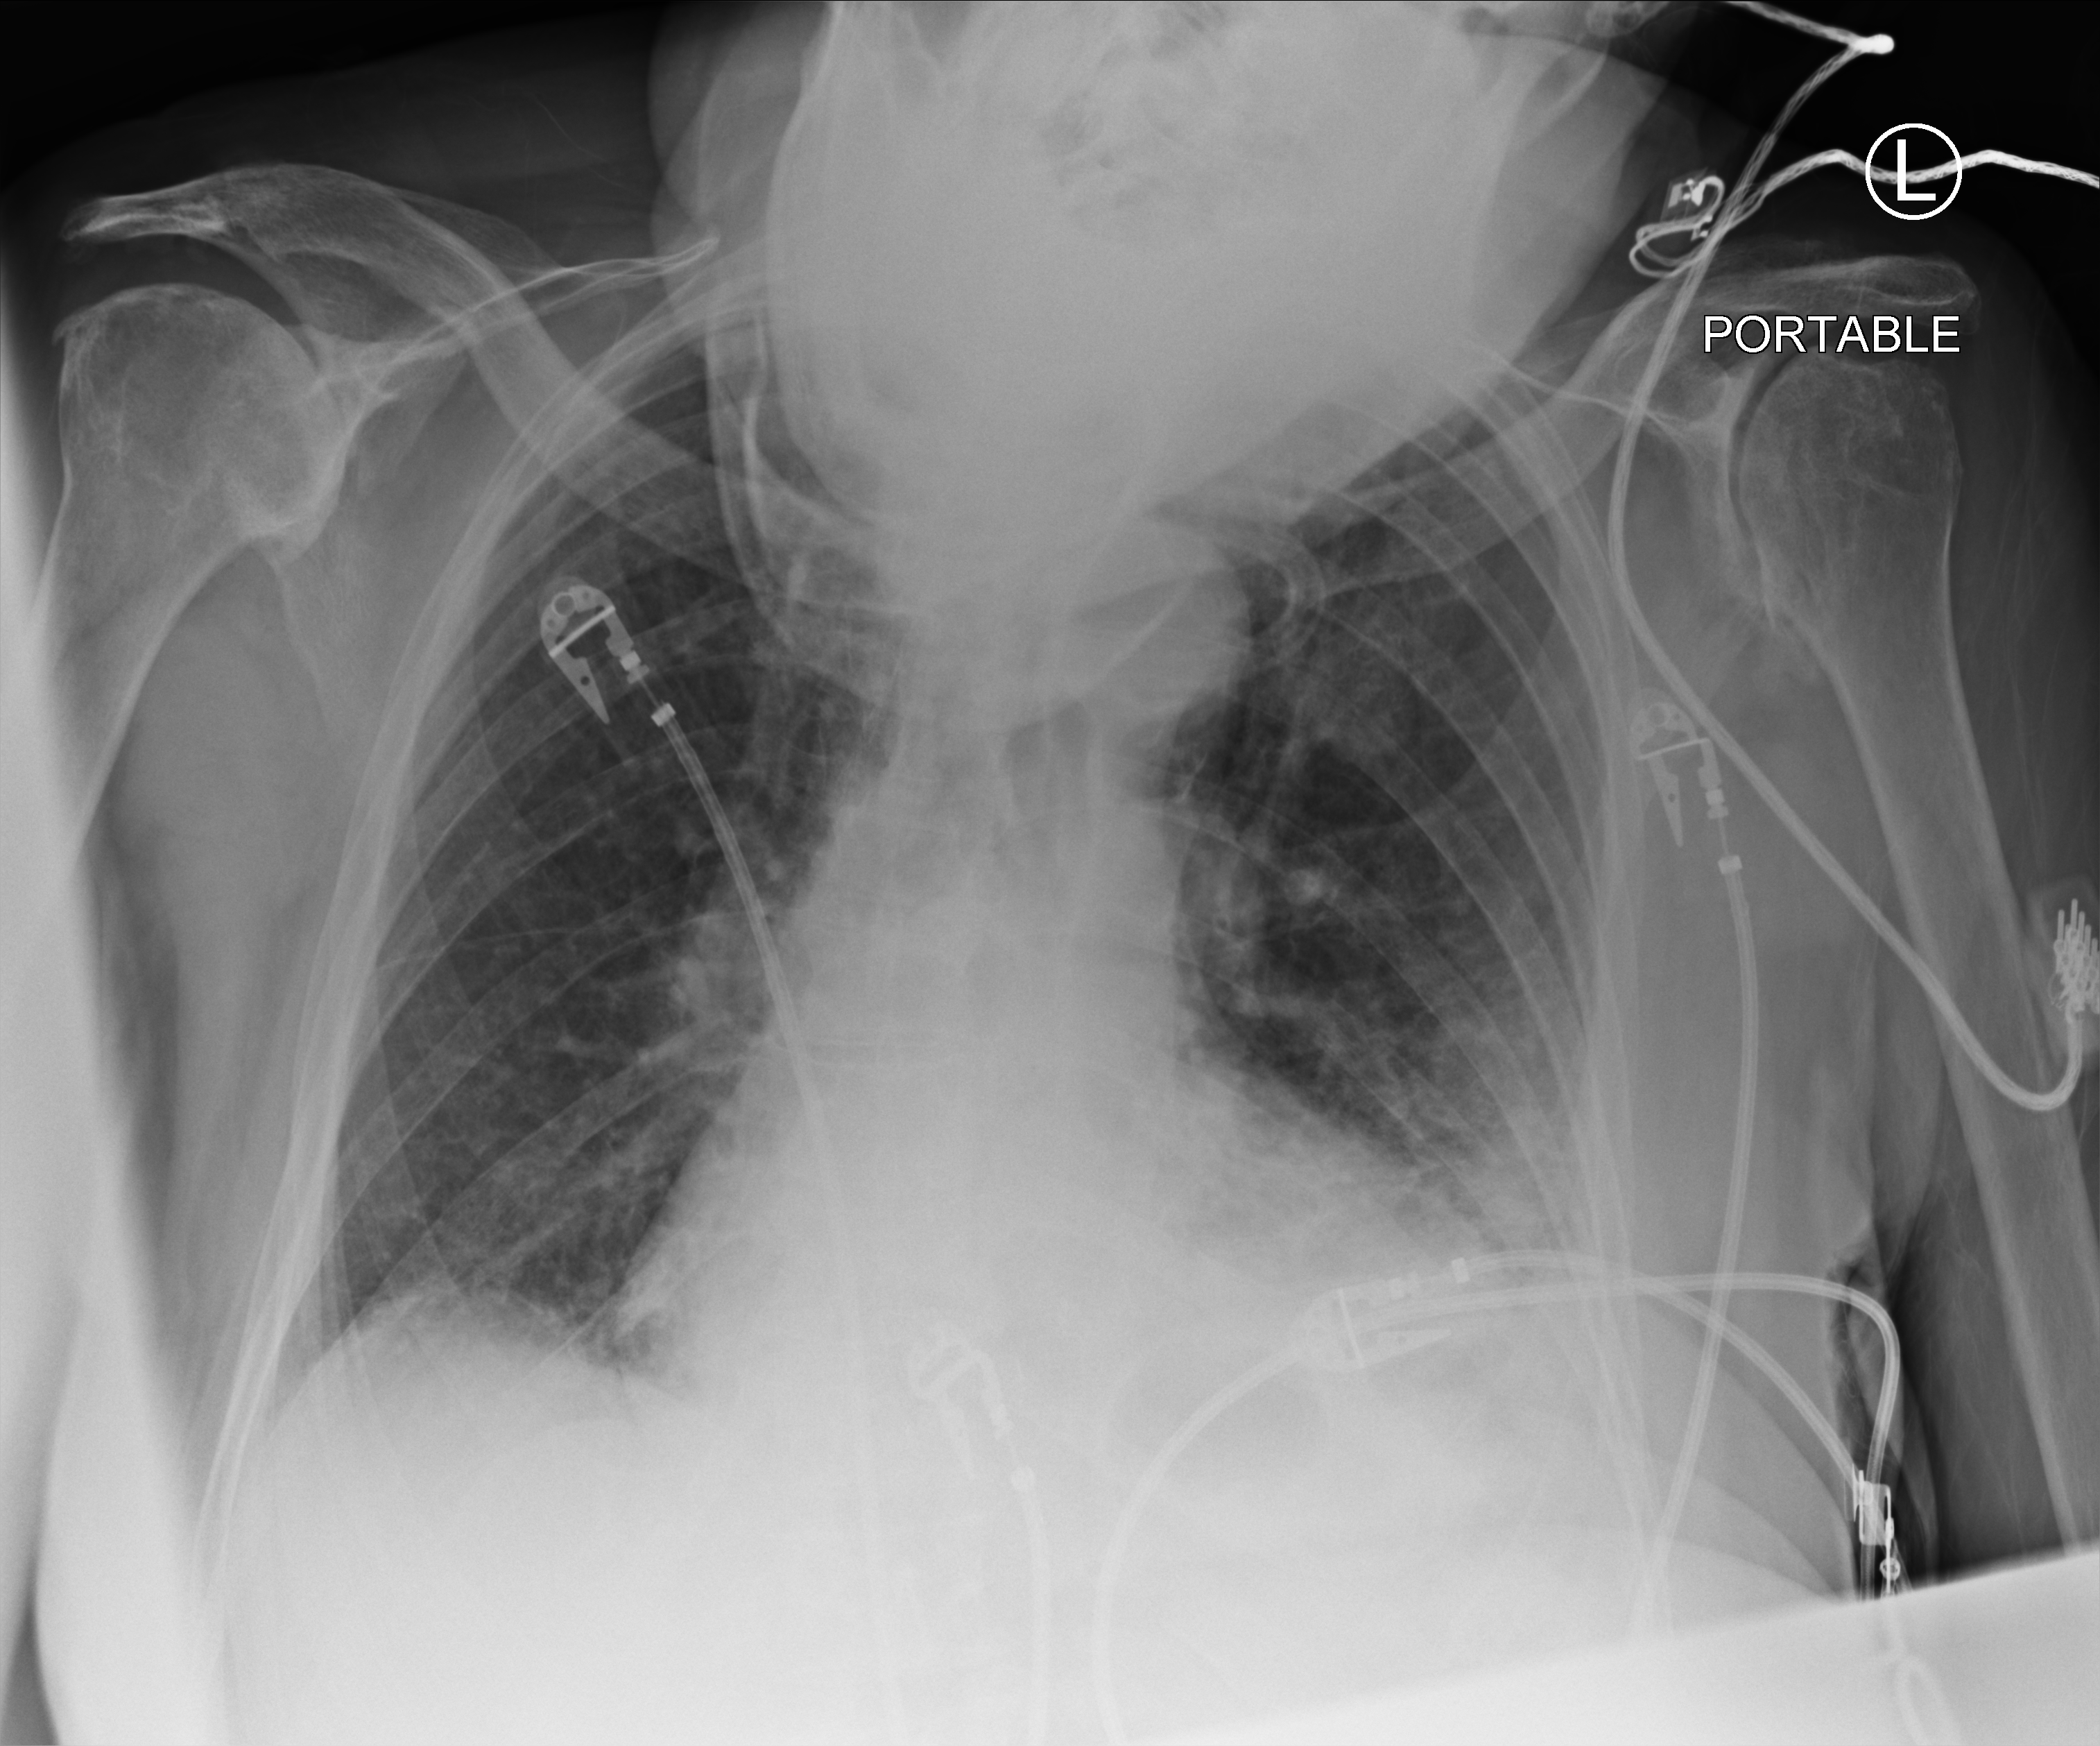
Portable chest radiograph. Patient hospitalised with COVID-19; male, aged 75–90 years.
Admission-level facts for this patient (not findings on this image; timing relative to this image not recorded): length of hospital stay: 17 days; mechanically ventilated during this hospital stay: no.